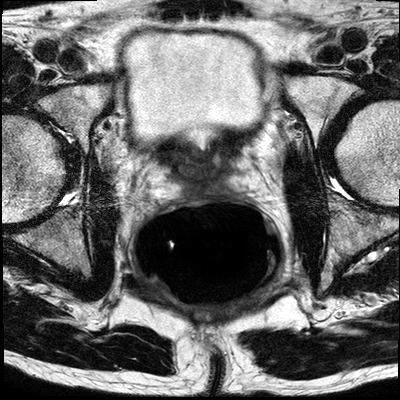
Multiparametric prostate MRI examination; 3 images, each a single mid-volume slice chosen by position (not for content). Treatment context recorded for this patient: No surgery, patient wanted to go for RT, treatment plan has to be decided.
Image 1: T2-weighted axial slice, slice 10 of 19, 4 mm slice thickness.
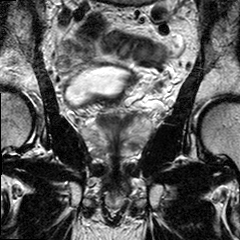
Image 2: T2-weighted coronal slice, series "T2W_TSE_COR", slice 13 of 24, 3 mm slice thickness.
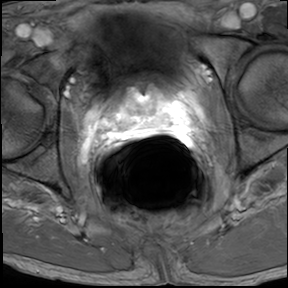
Image 3: DCE (dynamic gadolinium-enhanced) axial slice, slice 13 of 25, dynamic phase 5 of 8, 6 mm slice thickness.
MRI report (verbatim):
PSA level 20; Extracapsular disease assessment.
Pre-planning MRI FINDINGS: The prostate measures in the transverse diameter 5 cm, in the AP diameter 3 cm and the CC diameter 3.7 cm. The estimated gland volume therefore approximately 29 cc. Zonal anatomy is preserved. In the left posterior lateral peripheral zone of the apical third of the prostate at 4-5 o'clock, there is a 8 x 11 x 7 mm T2 hypo intense nodule seen Slightly below this nodule 3 mmm more apical, there is a 2nd T2 hypointense more geographic area seen measuring 13 x 5 x 4 mm between 5 and 7 o'clock prior median in the posterior peripheral zone. Post areas extends to the capsule however no extension beyond the capsule is seen. No suspicious enhancement beyond the capsule. Both neurovascular bundles are uninvolved. No evidence of seminal vesicle infiltration. No enlarged lymph nodes of the obturator or lilac stations.IMPRESSION: Bilateral prostate cancer predominantly in the lower third (apical) of the prostate, within the left posterio-lateral and bilateral paramedian posterior peripheral zones (from 4-7 o'clock) without evidence of extracapsular disease. No evidence of seminal vesicles infiltration or pelvic lymphadenopathy.

Biopsy pathology report for this patient (as recorded):
Gross Description: The specimen is received in formalin in a single container labeled with the patient's name, hospital number and "Prostate Biopsies". The specimen consists of multiple fragments of tan core biopsies measuring in length from 1.0 cm to 2.0 cm and 0.1 cm in diameter each. The specimen is submitted in toto in seven cassettes as follows: 1 right PZ, 2 right PZ/TZ, 3 right apex, 4 left PZ, 5 left PZ/TZ, 6 left apex, and 7 - floater. RIGHT PZ: PROSTATIC ADENOCARCINOMA GLEASON SCORE 3+3=6/10 INVOLVING <5% (ONE CORE) OF TISSUE REPRESENTED. 2. RIGHT PZ/TZ: PROSTATIC ADENOCARCINOMA GLEASON SCORE 3+3=6/10 INVOLVING 60% (TWO CORES) OF TISSUE REPRESENTED. 3. RIGHT APEX: BENIGN PROSTATIC TISSUE. NO TUMOR IDENTIFIED. 4. LEFT PZ: PROSTATIC ADENOCARCINOMA GLEASON SCORE 3+3=6/10 INVOLVING 15% (THREE CORES) OF TISSUE REPRESENTED. 5. LEFT PZ/TZ: PROSTATIC ADENOCARCINOMA GLEASON SCORE 3+3=6/10 INVOLVING 20% (ONE CORE) OF TISSUE REPRESENTED. 6. LEFT APEX: FIBROMUSCULAR TISSUE. NO TUMOR IDENTIFIED.7. FLOATER: PROSTATIC ADENOCARCINOMA GLEASON SCORE 3+3=6/10 INVOLVING <5% (ONE CORE) OF TISSUE REPRESENTED.